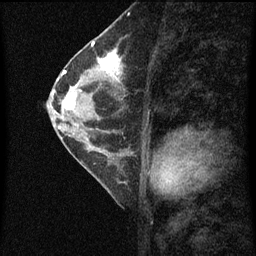
Breast MRI (dynamic contrast-enhanced), one sagittal slice; dynamic contrast-enhanced series, image 2 of 4 at this slice position (ordered by acquisition); 1.5 T; TE 4.2 ms, TR 8 ms; 2 mm slice thickness; 256 × 256 image matrix. Female patient, age 56 years.
Structures marked on this image (semi-automatically segmented with operator editing):
- analysis volume of interest (the breast-tissue region the enhancement analysis was run in; not a lesion): bounding box <56,52,127,115> (left, top, right, bottom; pixels)
- tumour enhancement mask (voxels above the 70 % enhancement threshold inside the analysis volume of interest): <62,52,123,113>